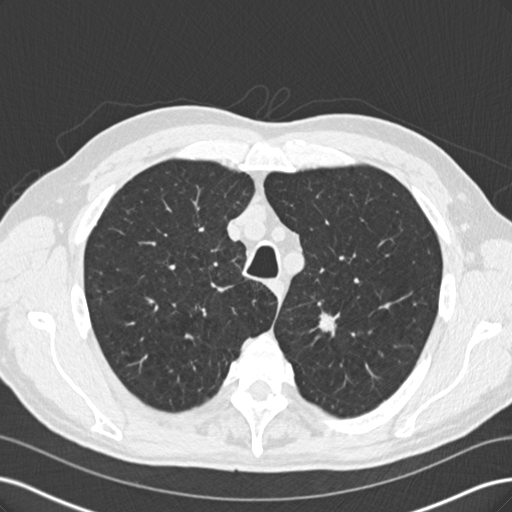
Low-dose screening chest CT, one axial slice. Reconstruction kernel B30f. 120 kVp. Lung window (W 1500 / L -600 HU). 2 mm slice thickness. 512 × 512 image matrix, field of view 360 × 360 mm.
Structures marked on this image (outlined manually by an expert reader):
- lesion 1 (tumor, upper lobe of left lung): bounding box (x1, y1, x2, y2) in pixels: (317, 311, 340, 332)